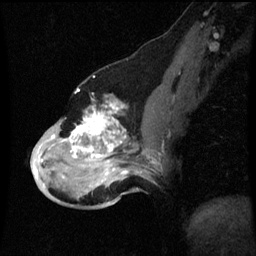
Breast MRI (dynamic contrast-enhanced), one sagittal slice. Position 29 of 60 along the scan axis. Dynamic contrast-enhanced series, image 2 of 3 at this slice position (ordered by acquisition). 1.5 T. TE 4.2 ms, TR 8.9 ms. 2 mm slice thickness. 256 × 256 image matrix. Female patient, age 49 years. From the clinical record (not read from this slice): setting: breast cancer imaged before/during neoadjuvant chemotherapy; receptor status: HR-positive, HER2-negative.
Structures marked on this image (semi-automatically segmented with operator editing):
- analysis volume of interest (the breast-tissue region the enhancement analysis was run in; not a lesion): box from (x=32, y=100) to (x=159, y=199) px
- tumour enhancement mask (voxels above the 70 % enhancement threshold inside the analysis volume of interest): (x=34, y=104)–(x=143, y=187)